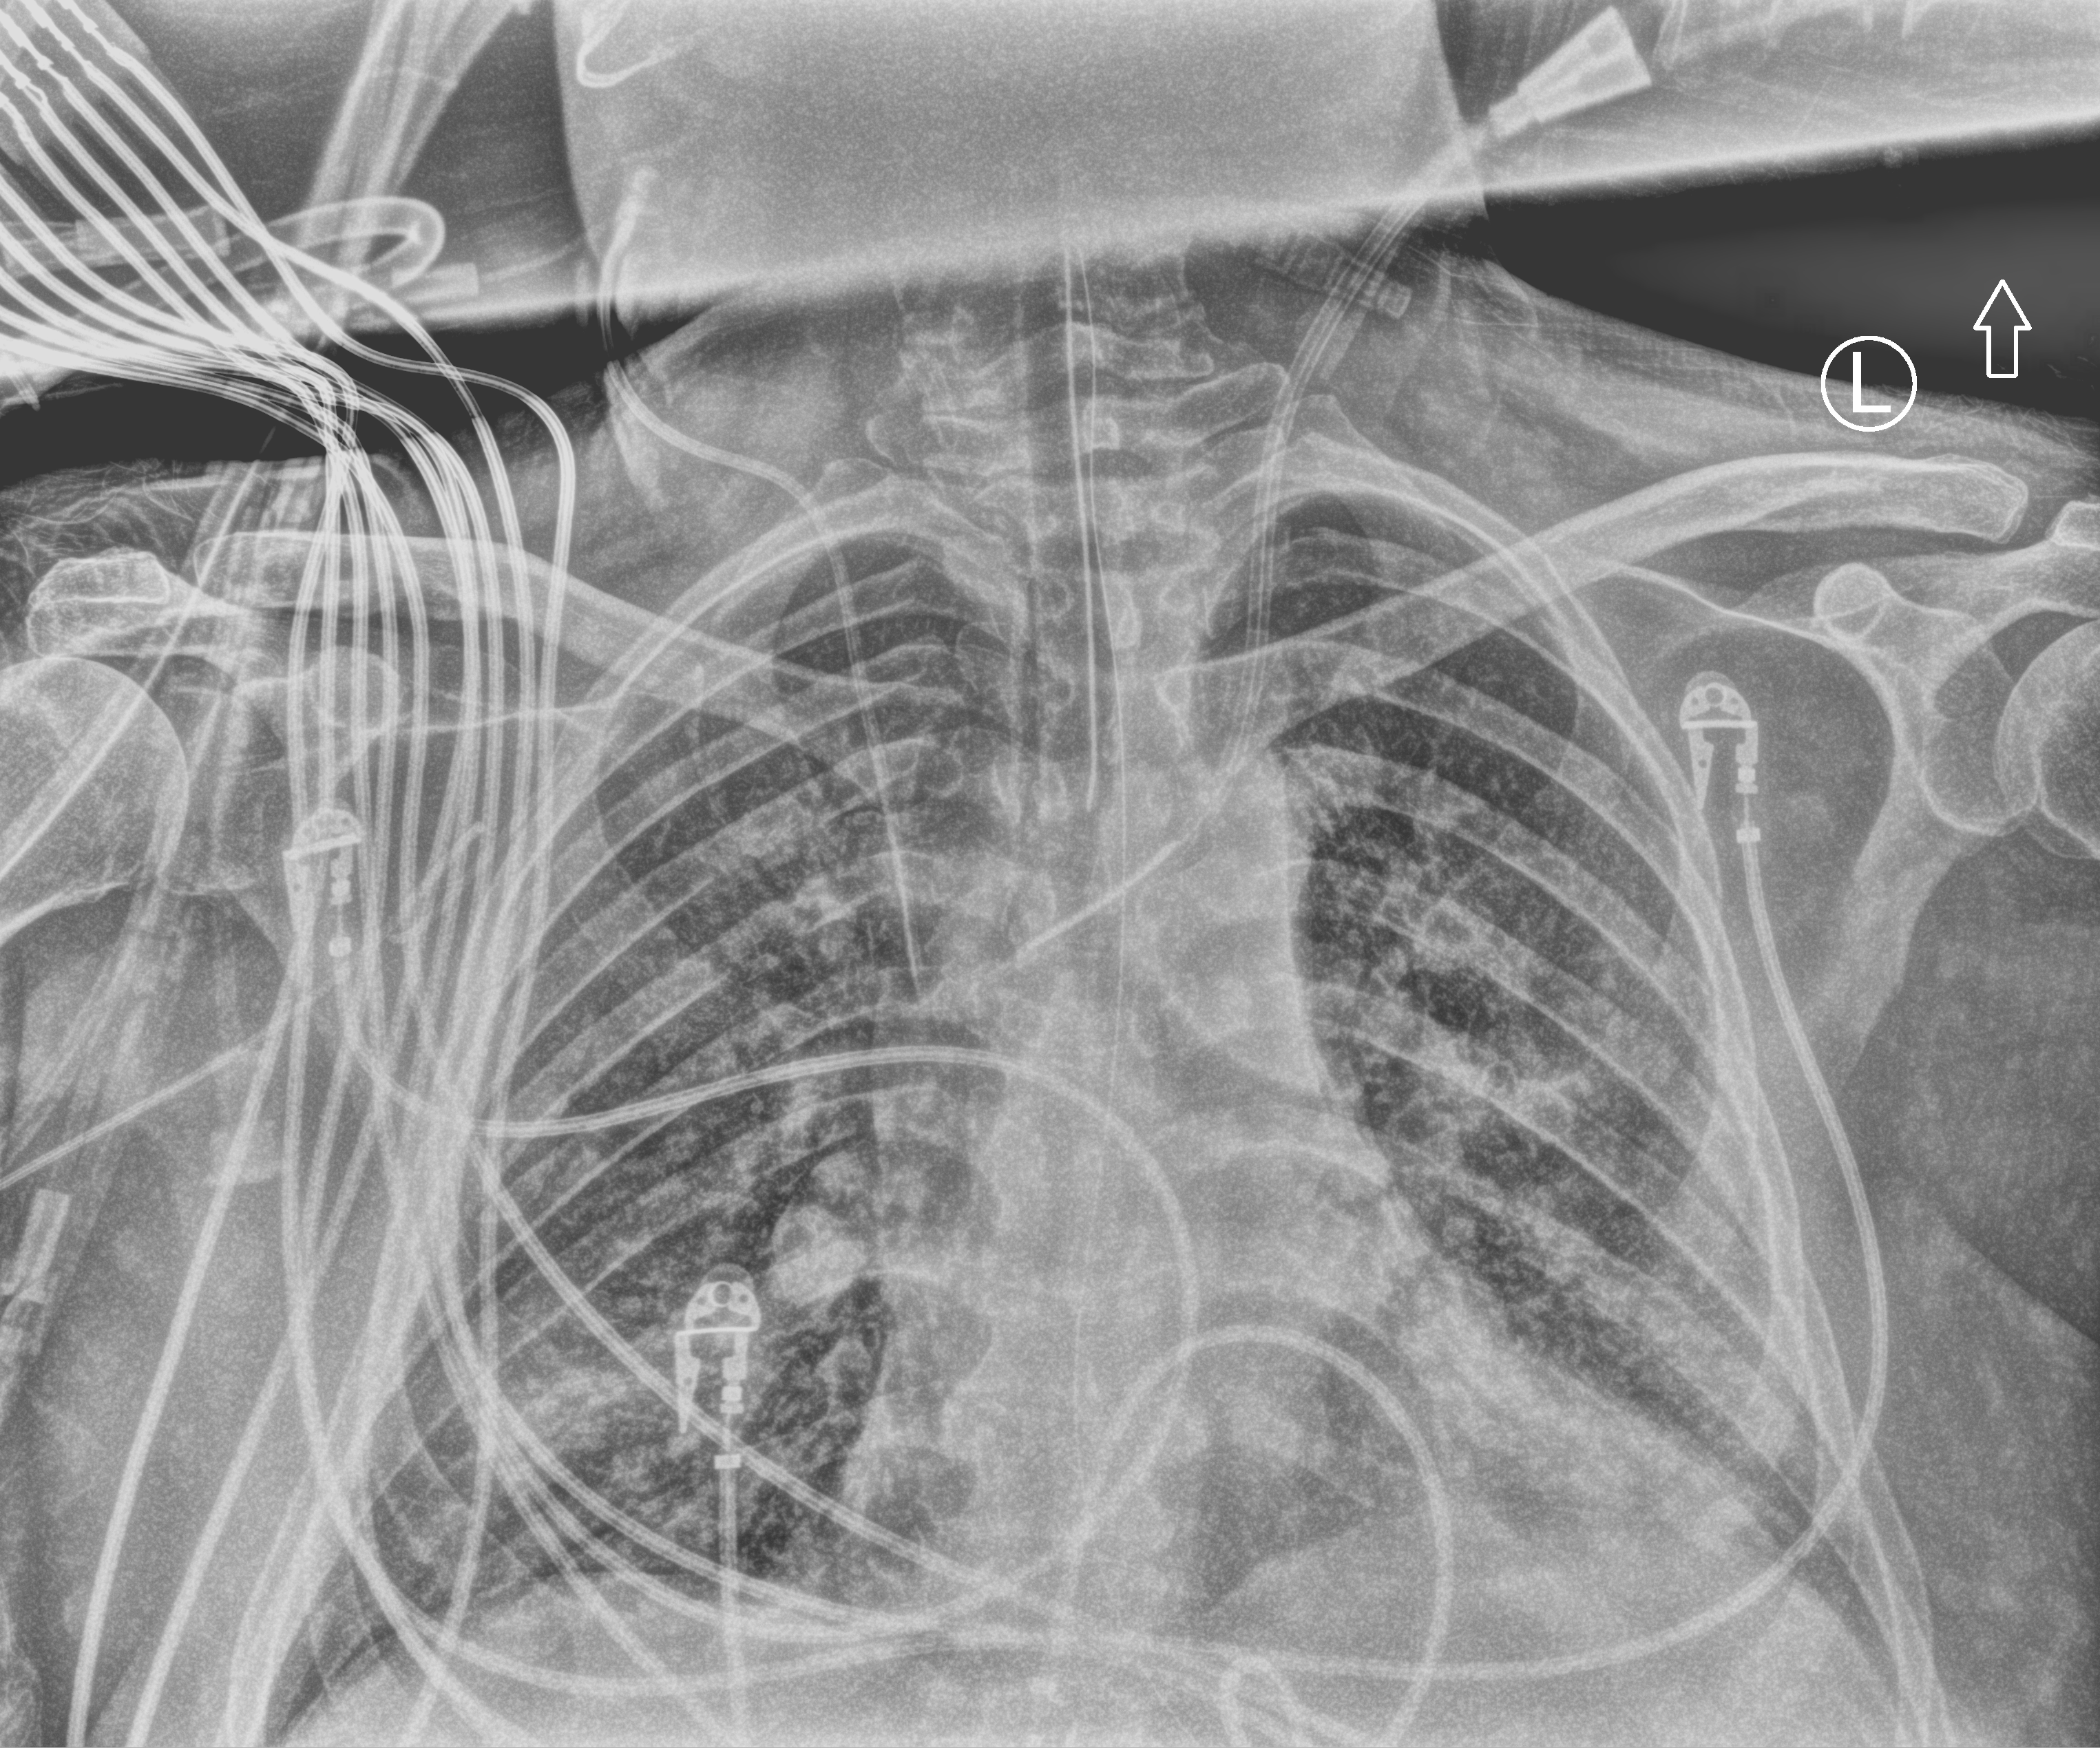
Portable chest radiograph, anteroposterior (AP) projection. Patient hospitalised with COVID-19; male, aged 18–59 years.
Admission-level facts for this patient (not findings on this image; timing relative to this image not recorded): mechanically ventilated during this hospital stay: yes.